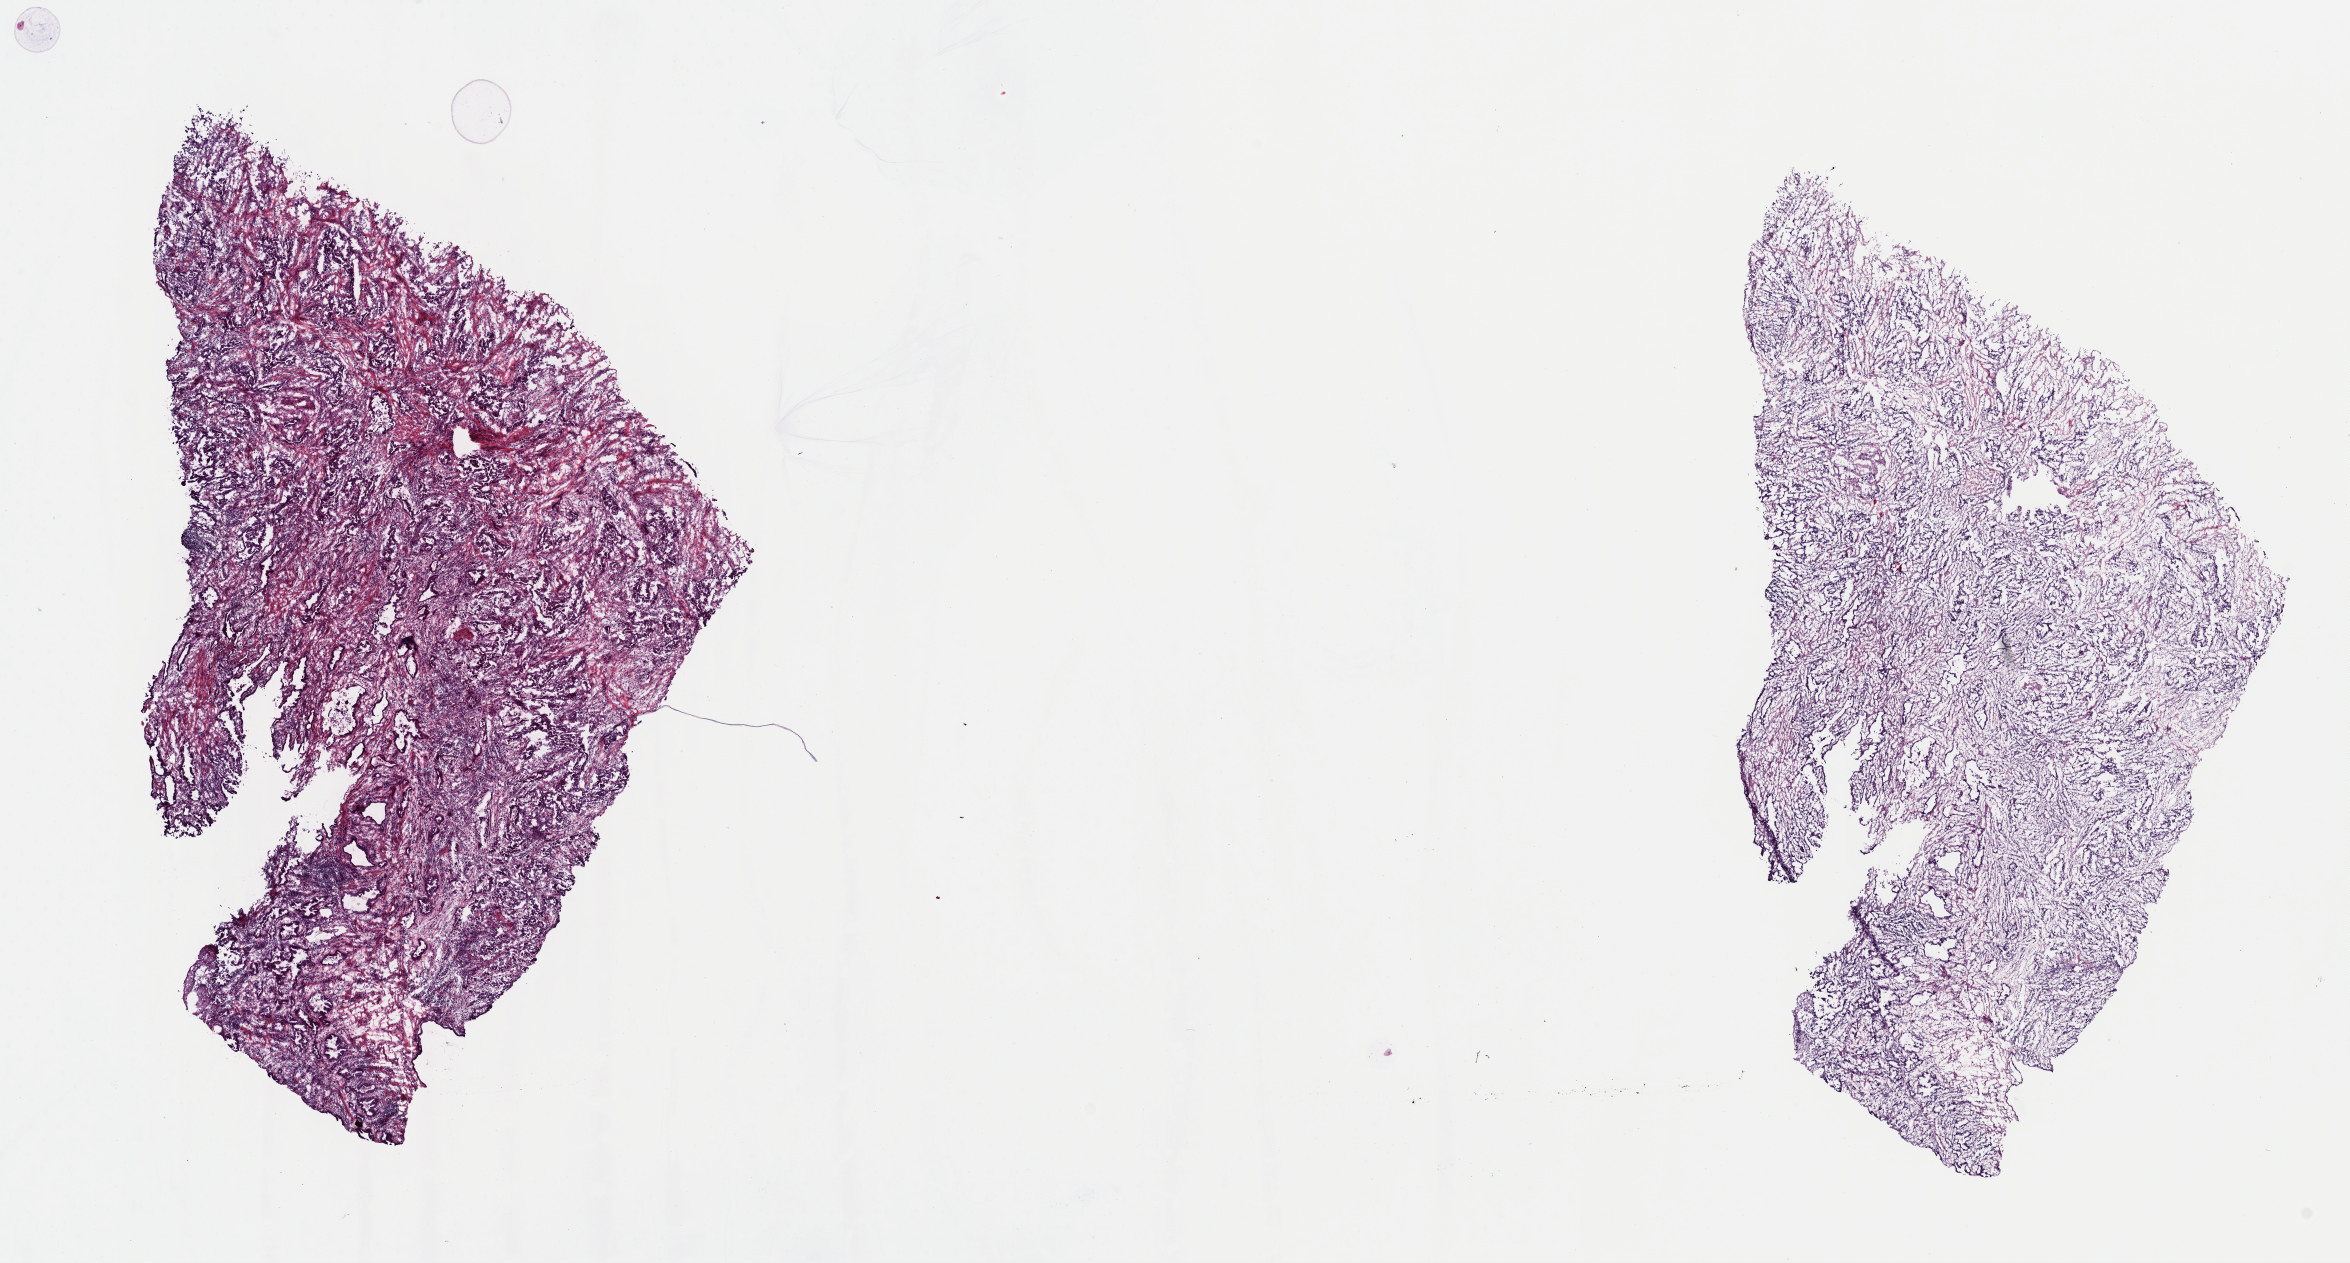
Hematoxylin and eosin (H&E) stained whole-slide image — low-resolution overview of the scanned area, about 18.6 x 10.0 mm (slide scanned at 40x); frozen section from the top of the tissue portion; primary tumour sample from the esophagus. Male, age 75 years at initial diagnosis. Histologic grade: G2 (moderately differentiated). Composition of this section per pathologist review: tumour cells 100%, tumour nuclei 65%, normal cells 0%, stromal cells 0%, necrosis 0%. Infiltration values recorded for this section: lymphocyte infiltration 5%, monocyte infiltration 0%, neutrophil infiltration 1%.
- AJCC pathologic stage: IIIC
- lymph nodes positive (case pathology): 21 of 37 examined
- histologic diagnosis: Adenocarcinoma, NOS (lower third of esophagus)